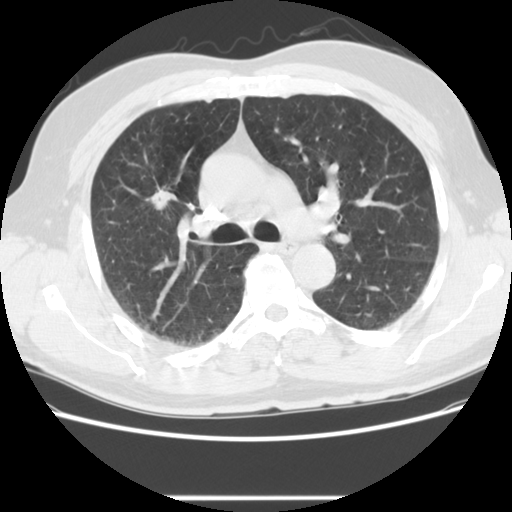
Low-dose screening chest CT, one axial slice. Slice 88 of 139 in the series (ordered by position). Reconstruction kernel STANDARD. Lung window (W 1500 / L -600 HU). 2.5 mm slice thickness. 512 × 512 image matrix, field of view 360 × 360 mm.
Structures marked on this image (outlined manually by an expert reader):
- lesion 1 (tumor, upper lobe of right lung): bounding box [x1, y1, x2, y2] px = [145, 188, 177, 210]